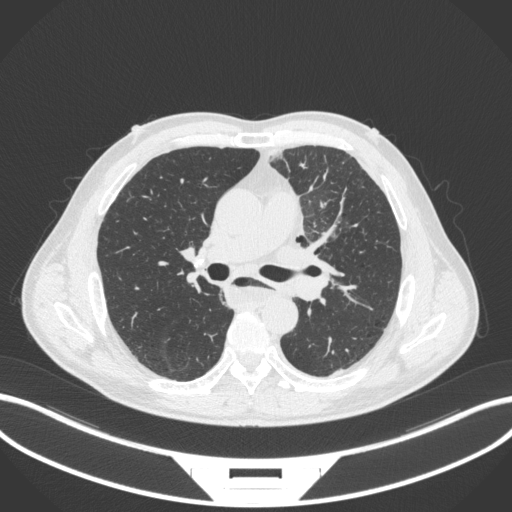
Chest CT, one axial slice. Reconstruction kernel B31f. 120 kVp. Lung window (W 1500 / L -600 HU). 1 mm slice thickness. 512 × 512 image matrix, field of view 400 × 400 mm. Male patient, age 57 years. Case-level facts recorded for this patient, not image findings: clinical TNM (as recorded): T2a N1 M0.
Structures marked on this image (rectangle marked by the reading radiologist):
- lung tumour (recorded histology: squamous cell carcinoma): box from (x=274, y=234) to (x=329, y=277) px